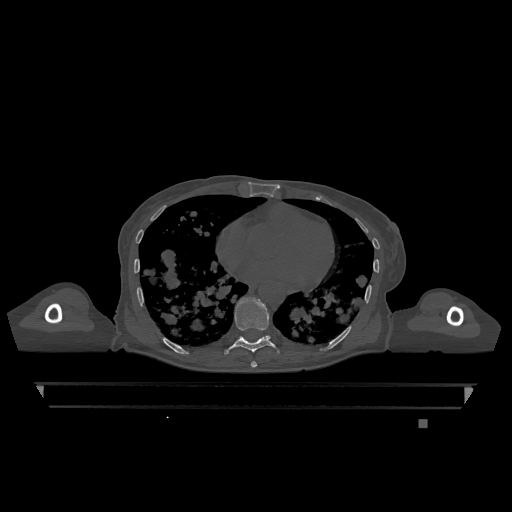
CT including the spine, one axial slice. Slice 687 of 1317 in the series (ordered by position). Bone window (W 1800 / L 400 HU). 0.5 mm slice thickness. 512 × 512 image matrix. Female patient, age 74 years. Case-level facts recorded for this patient, not image findings: primary cancer: lung; vertebrae with lytic lesions (as recorded): T1, T4, T5, T6, L4, L5.
Outlined on this slice (semi-automatically segmented with operator editing):
- T7 vertebra: box from (x=251, y=361) to (x=257, y=368) px
- T9 vertebra: (x=224, y=297)–(x=280, y=355)